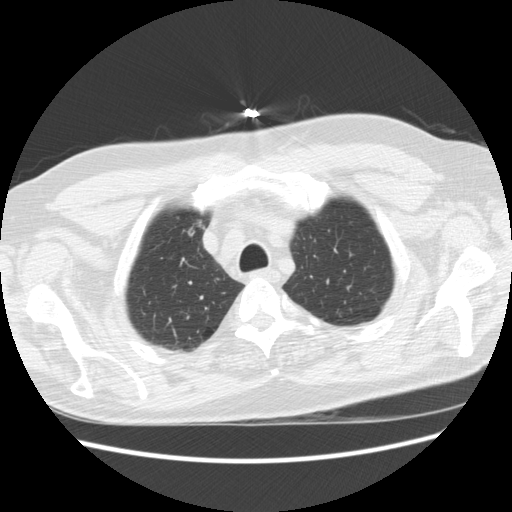
Low-dose screening chest CT, axial slice. First (baseline) screen. Lung window (W 1500 / L -600 HU). Standard (soft-tissue) reconstruction kernel (STANDARD). 120 kVp. Male participant, aged 66 years at enrolment. Former smoker at enrolment.
• Expert-annotated lung lesion, bounding box [x1, y1, x2, y2] px = [172, 211, 210, 248].
• Screening reader's record for this exam: no non-calcified nodule ≥4 mm recorded.
• Official screen result: negative screen, significant abnormalities not suspicious for lung cancer.
• Later outcome: lung cancer diagnosed 951 days after this screen — bronchiolo-alveolar adenocarcinoma, NOS, right upper lobe, moderately differentiated (G2), stage IA (AJCC 6th edition), 12 mm at pathology.